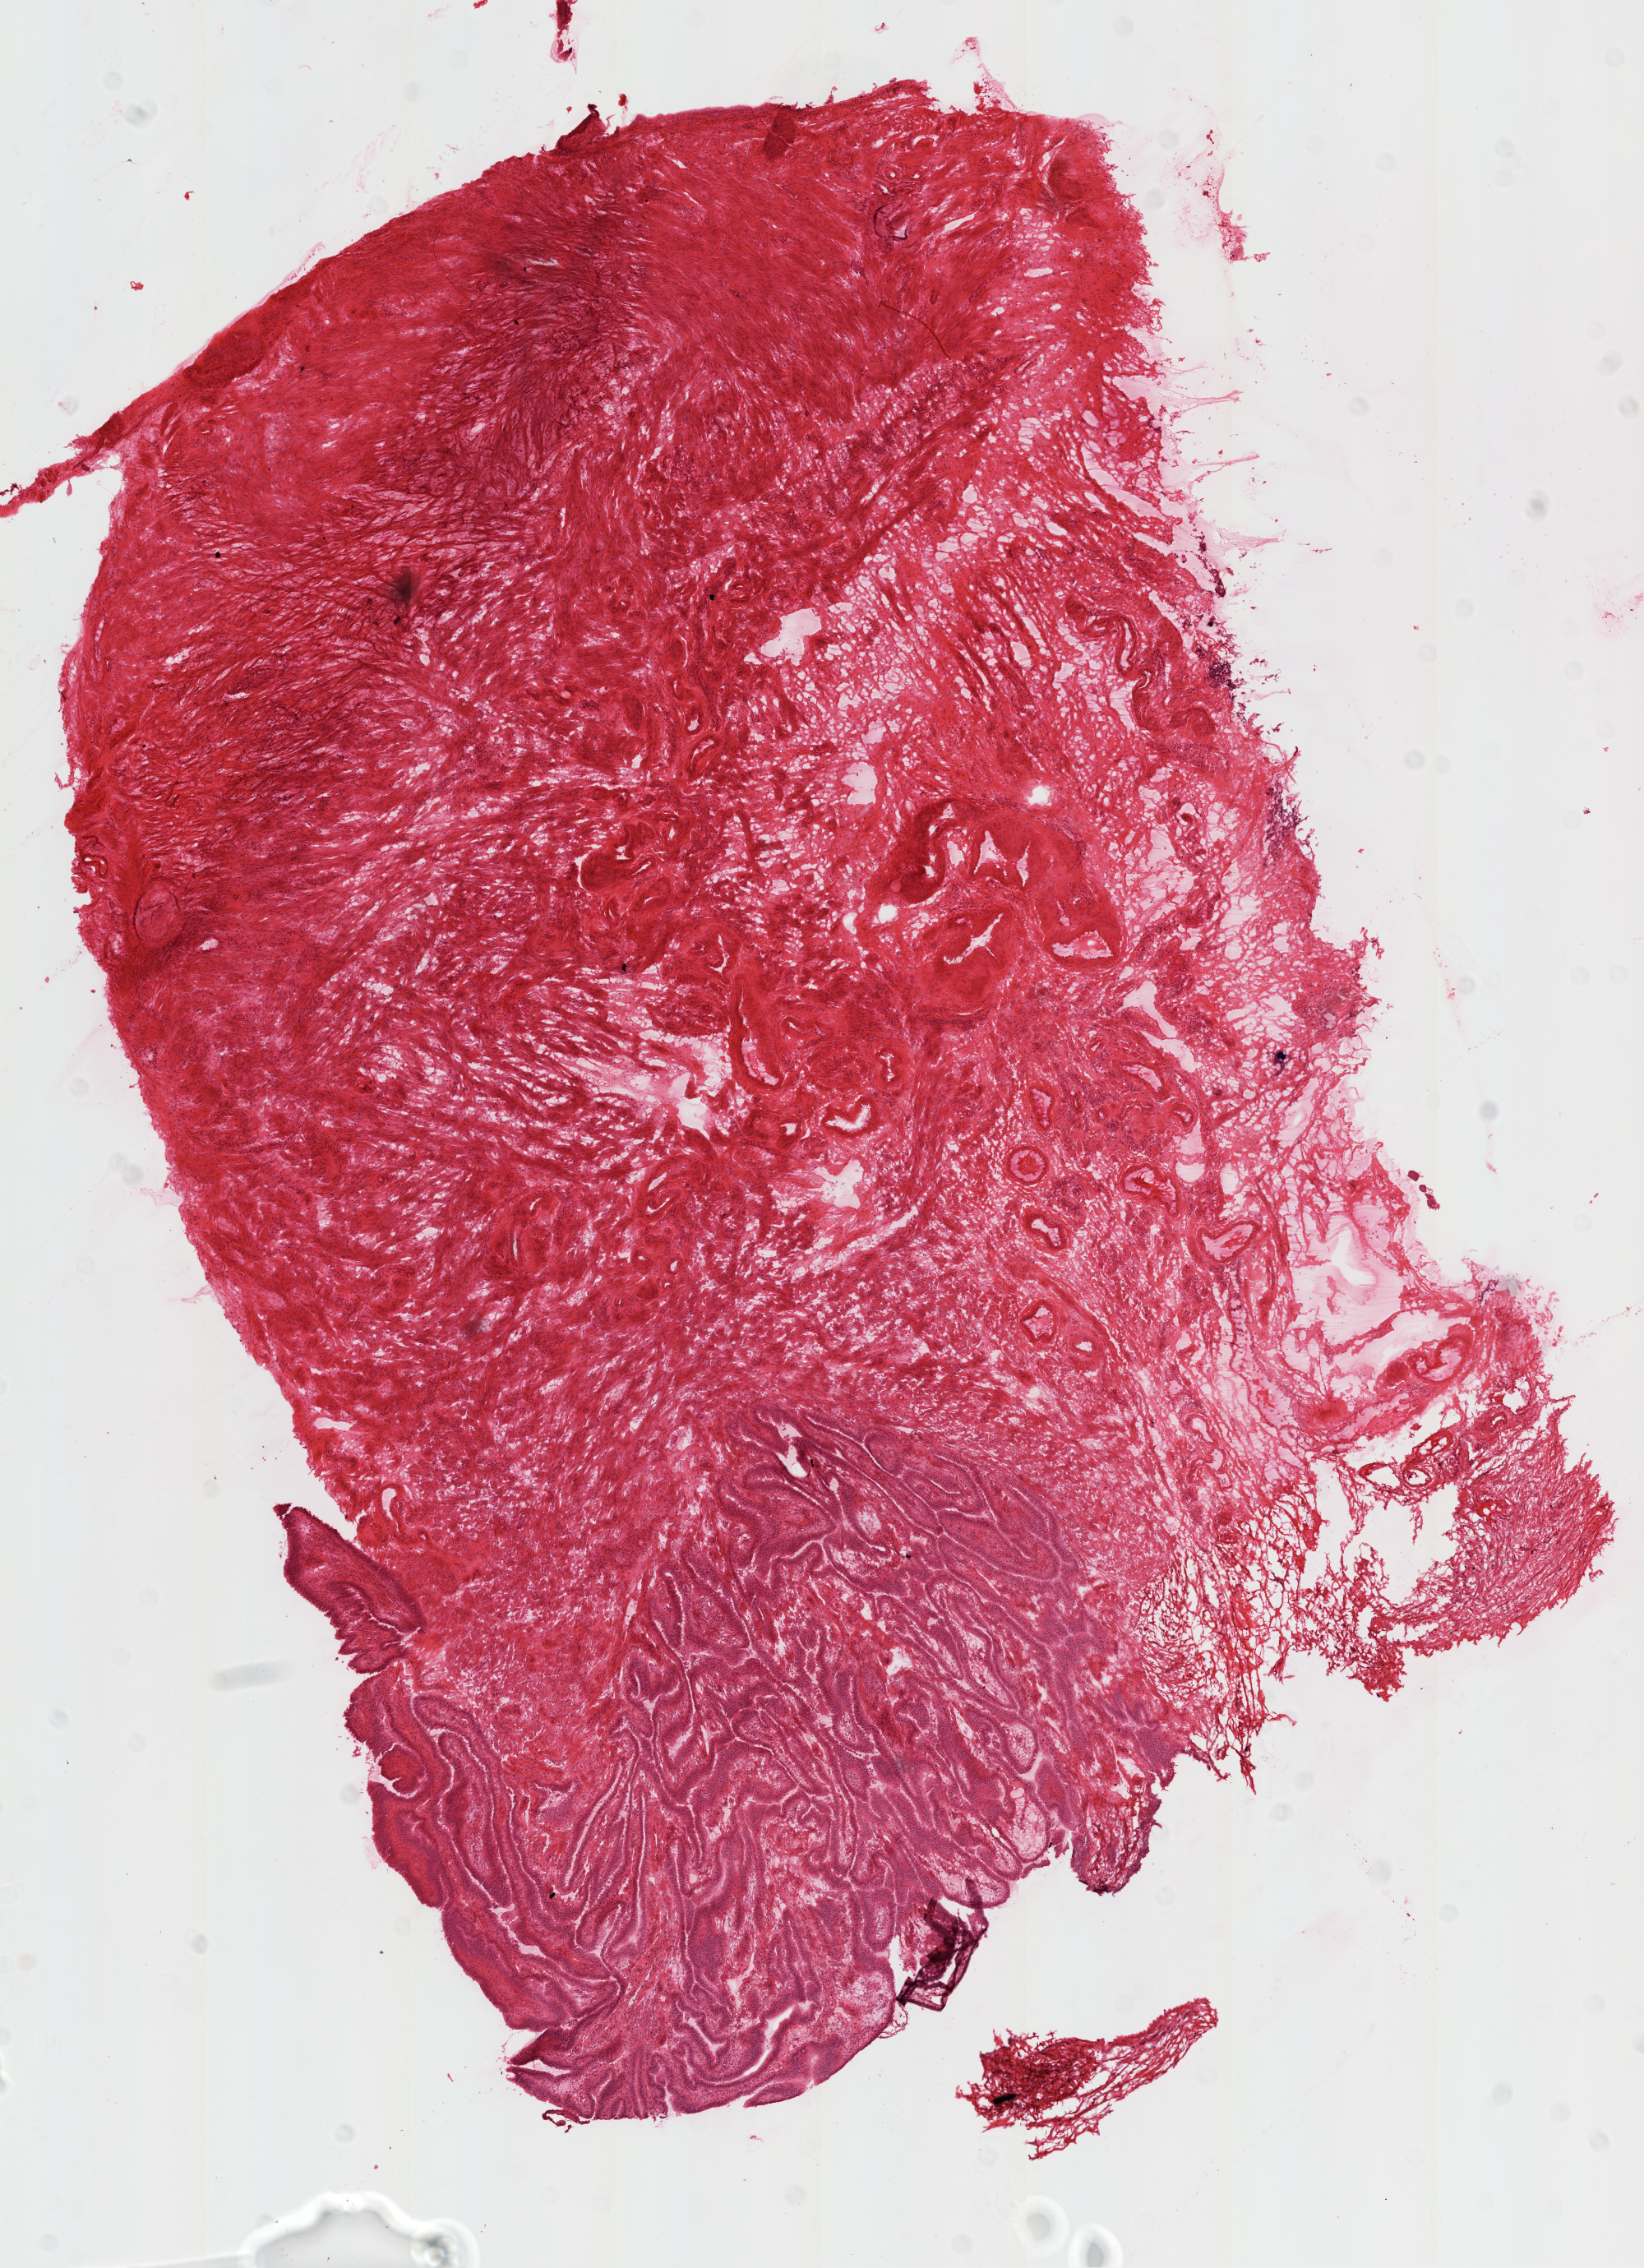
Whole-slide histology image, H&E, a low-resolution overview of the entire scanned area, about 8.0 x 11.1 mm. Frozen section. Ovary, solid tissue normal (non-tumour tissue) sample. Patient: female, age at initial diagnosis 40 years.
- this section: solid tissue normal (non-tumour) sample from the same patient
- patient diagnosis: Serous cystadenocarcinoma, NOS